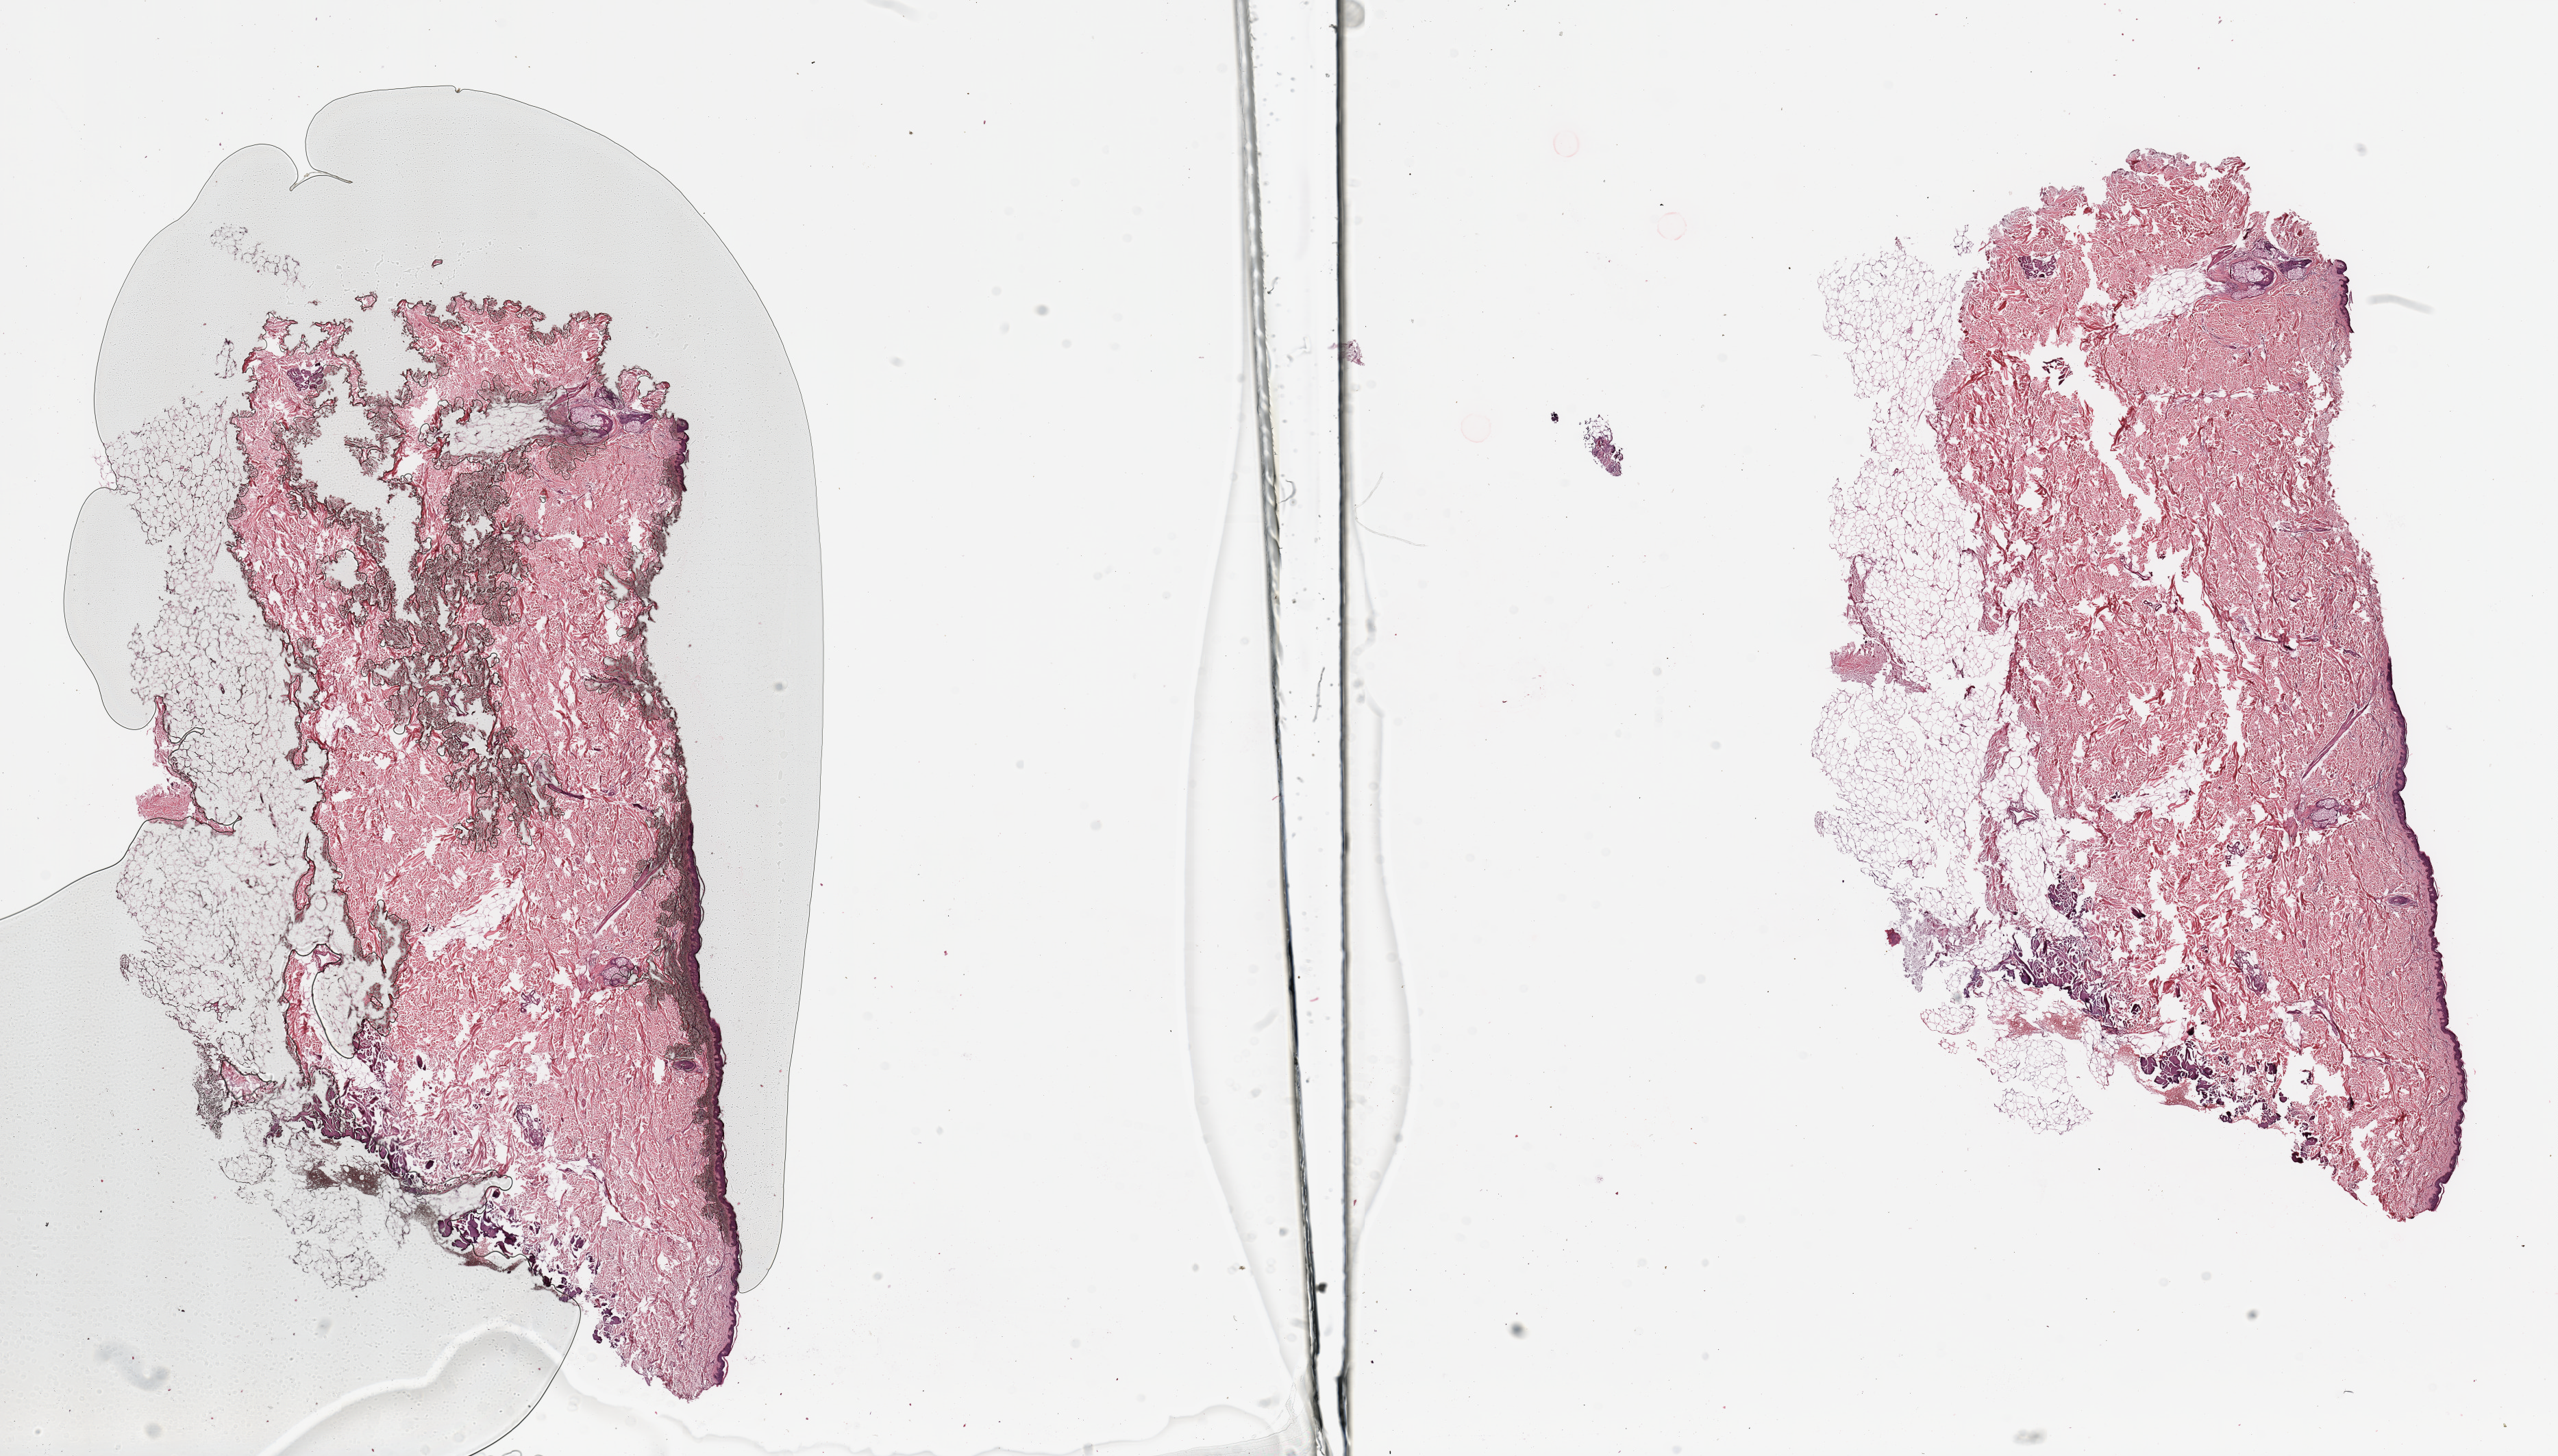
Whole-slide histology image, Hematoxylin and eosin (H&E) stained, low-resolution overview of the scanned area, about 29.5 x 16.8 mm (from a 20x scan). Normal (non-tumour) tissue sample. Female, 76 y/o.
• this section: normal (non-tumour) tissue from the same patient
• patient diagnosis (cohort enrolment): sarcoma (site not recorded at cohort level)